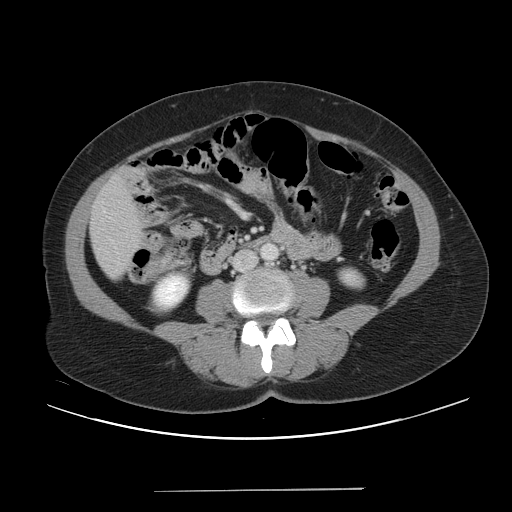
Contrast-enhanced abdominal CT, one axial slice; slice 7 of 56 in the series (ordered by position); intravenous contrast given; soft-tissue window (W 400 / L 40 HU); 5 mm slice thickness; 512 × 512 image matrix, field of view 419 × 419 mm. Female patient, age 54 years. From the clinical record (not read from this slice): diagnosis: colorectal cancer liver metastases, imaged before liver resection; multiple liver metastases: yes; largest metastasis: 3.2 cm; disease in both lobes: yes.
Structures marked on this image (expert manual segmentation):
- liver: bounding box [x1, y1, x2, y2] px = [91, 175, 141, 279]